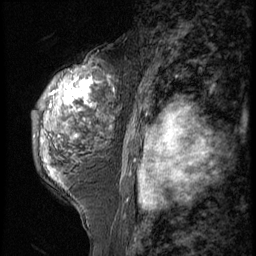
Breast MRI (dynamic contrast-enhanced), one sagittal slice; position 37 of 56 along the scan axis; 3 images stored at this slice position (order not interpretable as contrast timing); 1.5 T; TE 4.2 ms, TR 9 ms; 256 × 256 image matrix, field of view 180 × 180 mm. Patient: female, 50 years. From the clinical record (not read from this slice): setting: breast cancer imaged before/during neoadjuvant chemotherapy; receptor status: triple-negative.
Outlined on this slice (semi-automatically segmented with operator editing):
- analysis volume of interest (the breast-tissue region the enhancement analysis was run in; not a lesion): bounding box <31,50,123,191> (left, top, right, bottom; pixels)
- tumour enhancement mask (voxels above the 140 % enhancement threshold inside the analysis volume of interest): <66,81,96,108>